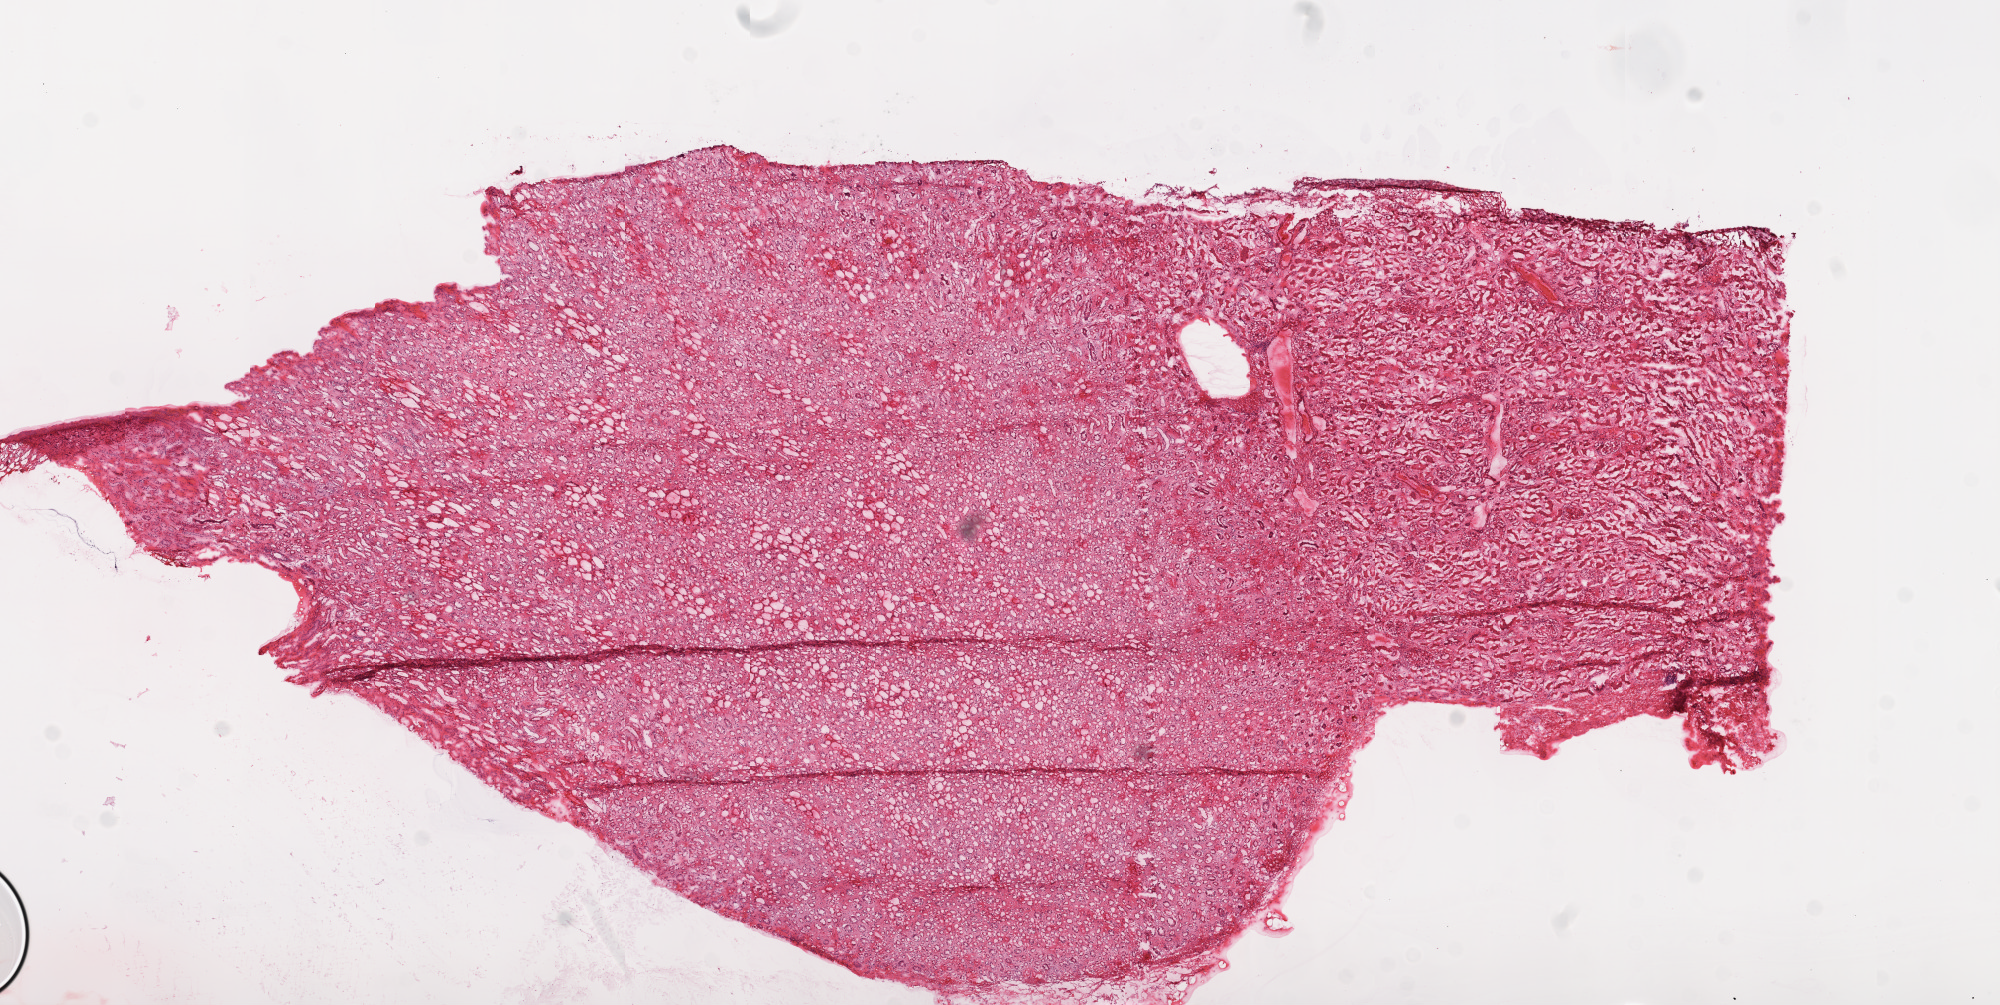
Hematoxylin and eosin (H&E) stained whole-slide image — a low-resolution overview of the entire scanned area, about 16.0 x 8.1 mm (slide scanned at 20x), frozen section, solid tissue normal (non-tumour tissue) sample from the kidney. Male patient; age at initial diagnosis 68 years.
This section: solid tissue normal sample (biorepository sample class). Patient diagnosis: Clear cell adenocarcinoma, NOS.